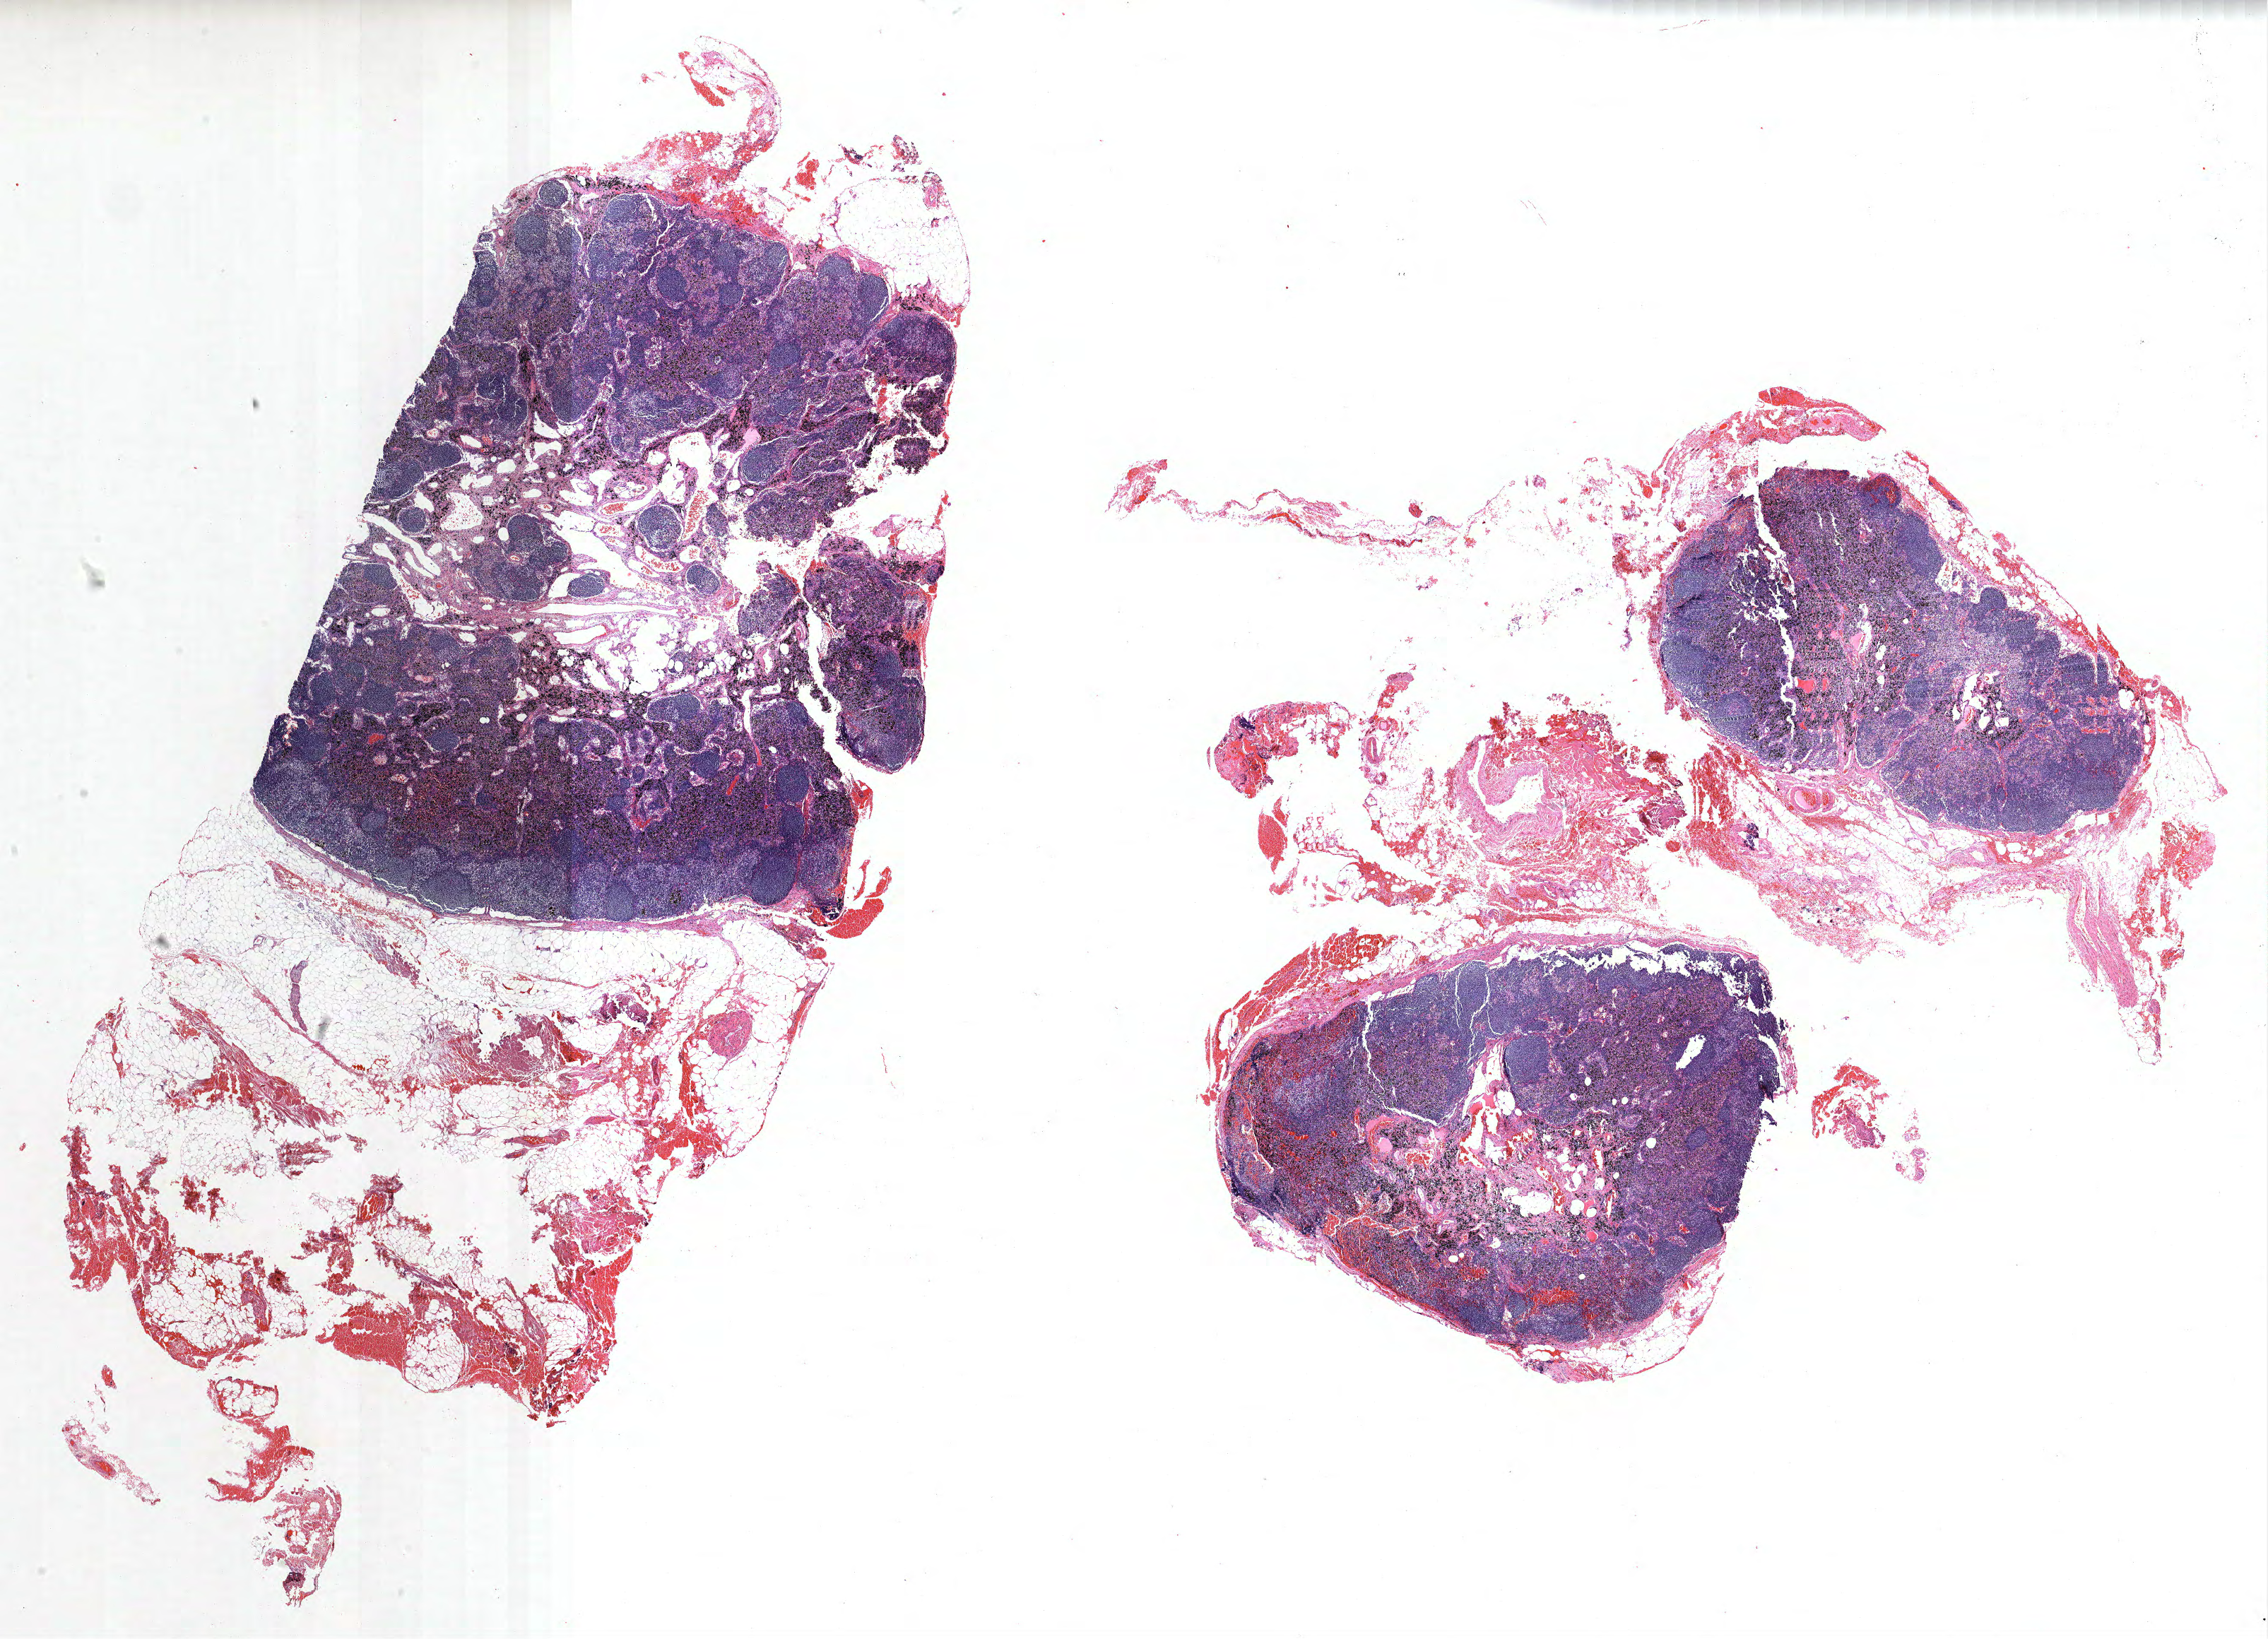
H&E-stained whole-slide image — low-resolution overview of the scanned area, about 25.7 x 18.6 mm, FFPE section, lung. Male, age 65 at enrolment. Former smoker at enrolment. Grade: moderately differentiated (G2).
Participant's lung-cancer diagnosis: Bronchiolo-alveolar adenocarcinoma, NOS (ICD-O-3 8250/3). Primary tumour location (clinical record): right upper lobe. Stage (AJCC 6th edition): IIA. Tumour size (pathology): 14 mm.